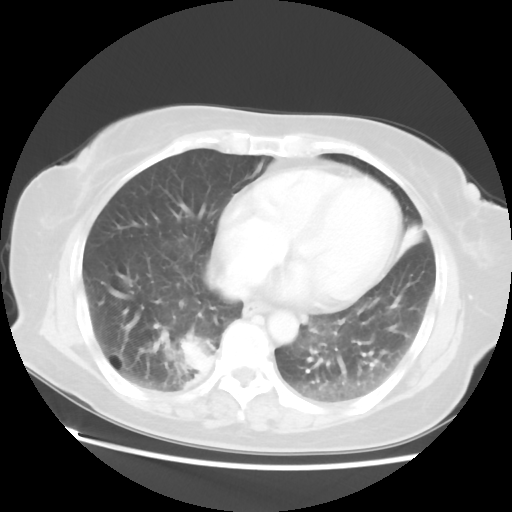
Chest CT, one axial slice; position 21 of 52 along the scan axis; reconstruction kernel STANDARD; 120 kVp; lung window (W 1500 / L -600 HU); 5 mm slice thickness; 512 × 512 image matrix. Patient: female, 69 years. From the clinical record (not read from this slice): clinical TNM (as recorded): T2 N1 M1a.
Outlined on this slice (rectangle marked by the reading radiologist):
- lung tumour (recorded histology: adenocarcinoma): bounding box <172,332,214,389> (left, top, right, bottom; pixels)